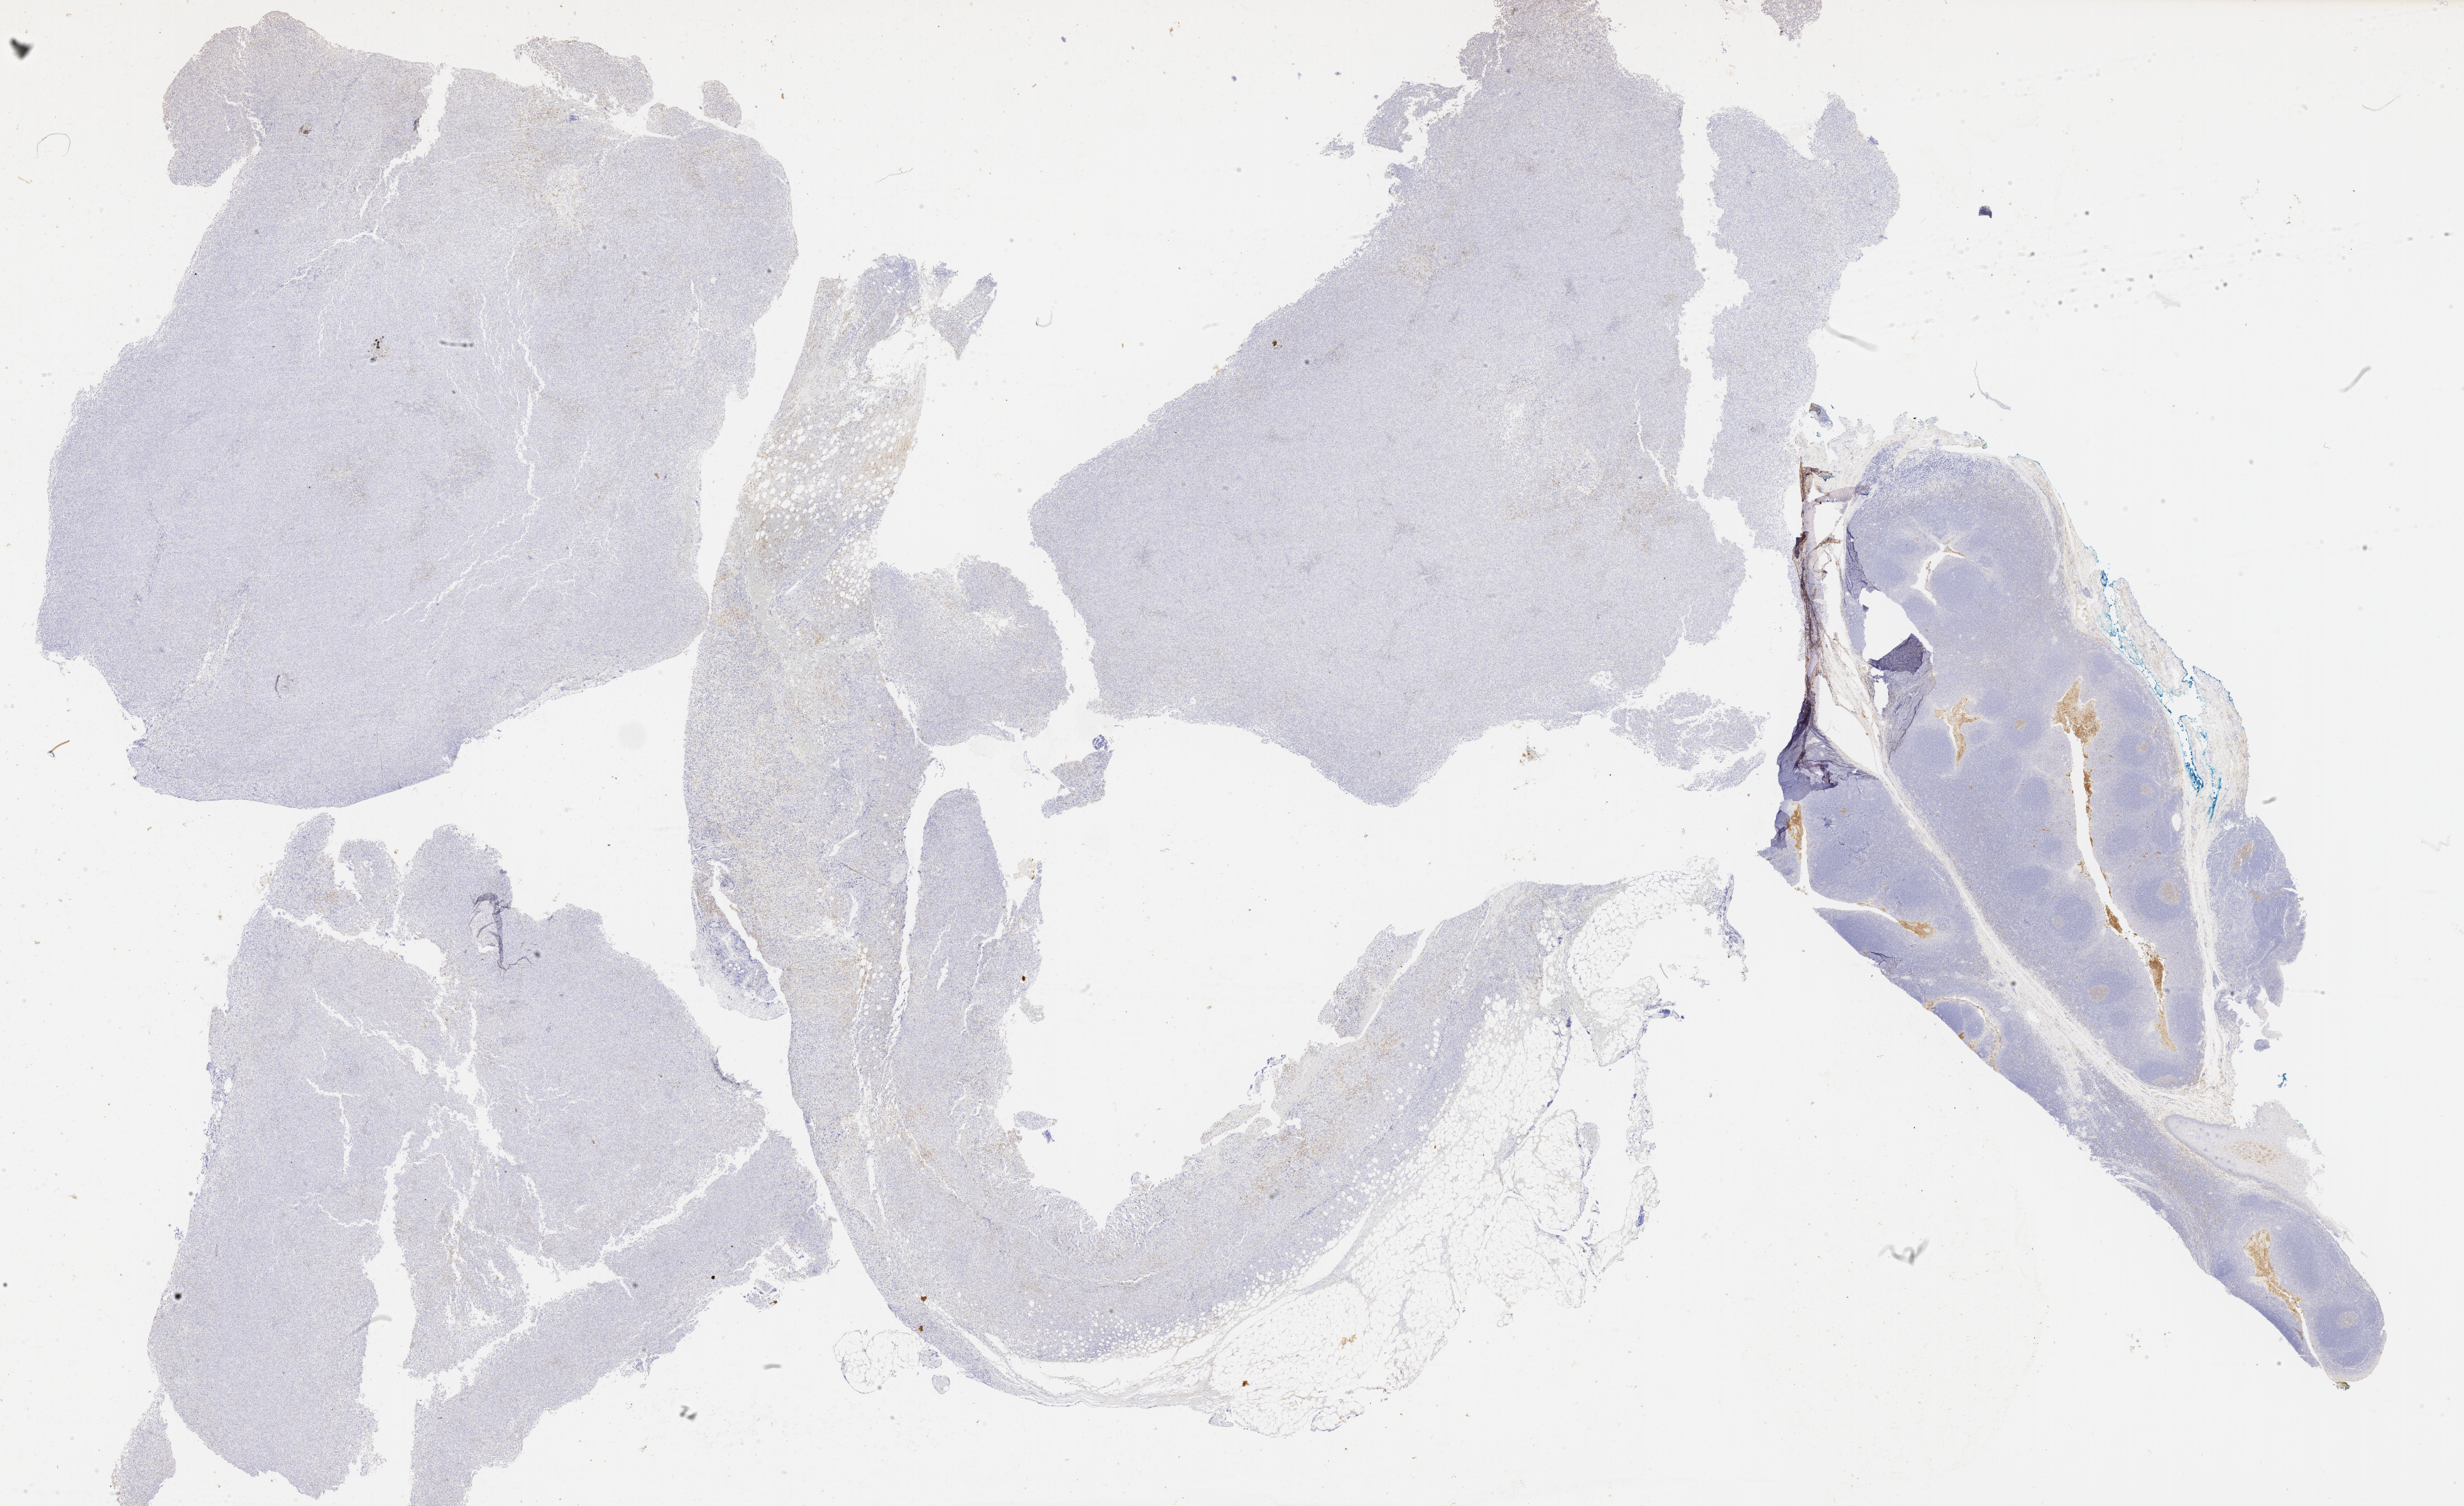
Immunohistochemistry (IHC) whole-slide image stained for CD10 — shown as a low-resolution overview of the whole scanned area (about 31.7 x 19.4 mm). Female patient.
Specimen: tumor tissue.